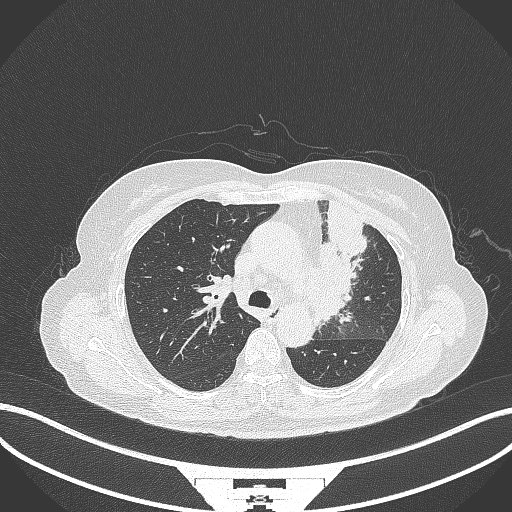
Chest CT, one axial slice; position 226 of 382 along the scan axis; reconstruction kernel B70f; 120 kVp; lung window (W 1500 / L -600 HU); 1 mm slice thickness; 512 × 512 image matrix. Patient: female, 64 years. From the clinical record (not read from this slice): clinical TNM (as recorded): T2a N2 M0.
Structures marked on this image (bounding box drawn by a radiologist):
- lung tumour (recorded histology: adenocarcinoma): bounding box [x1, y1, x2, y2] px = [305, 200, 368, 322]